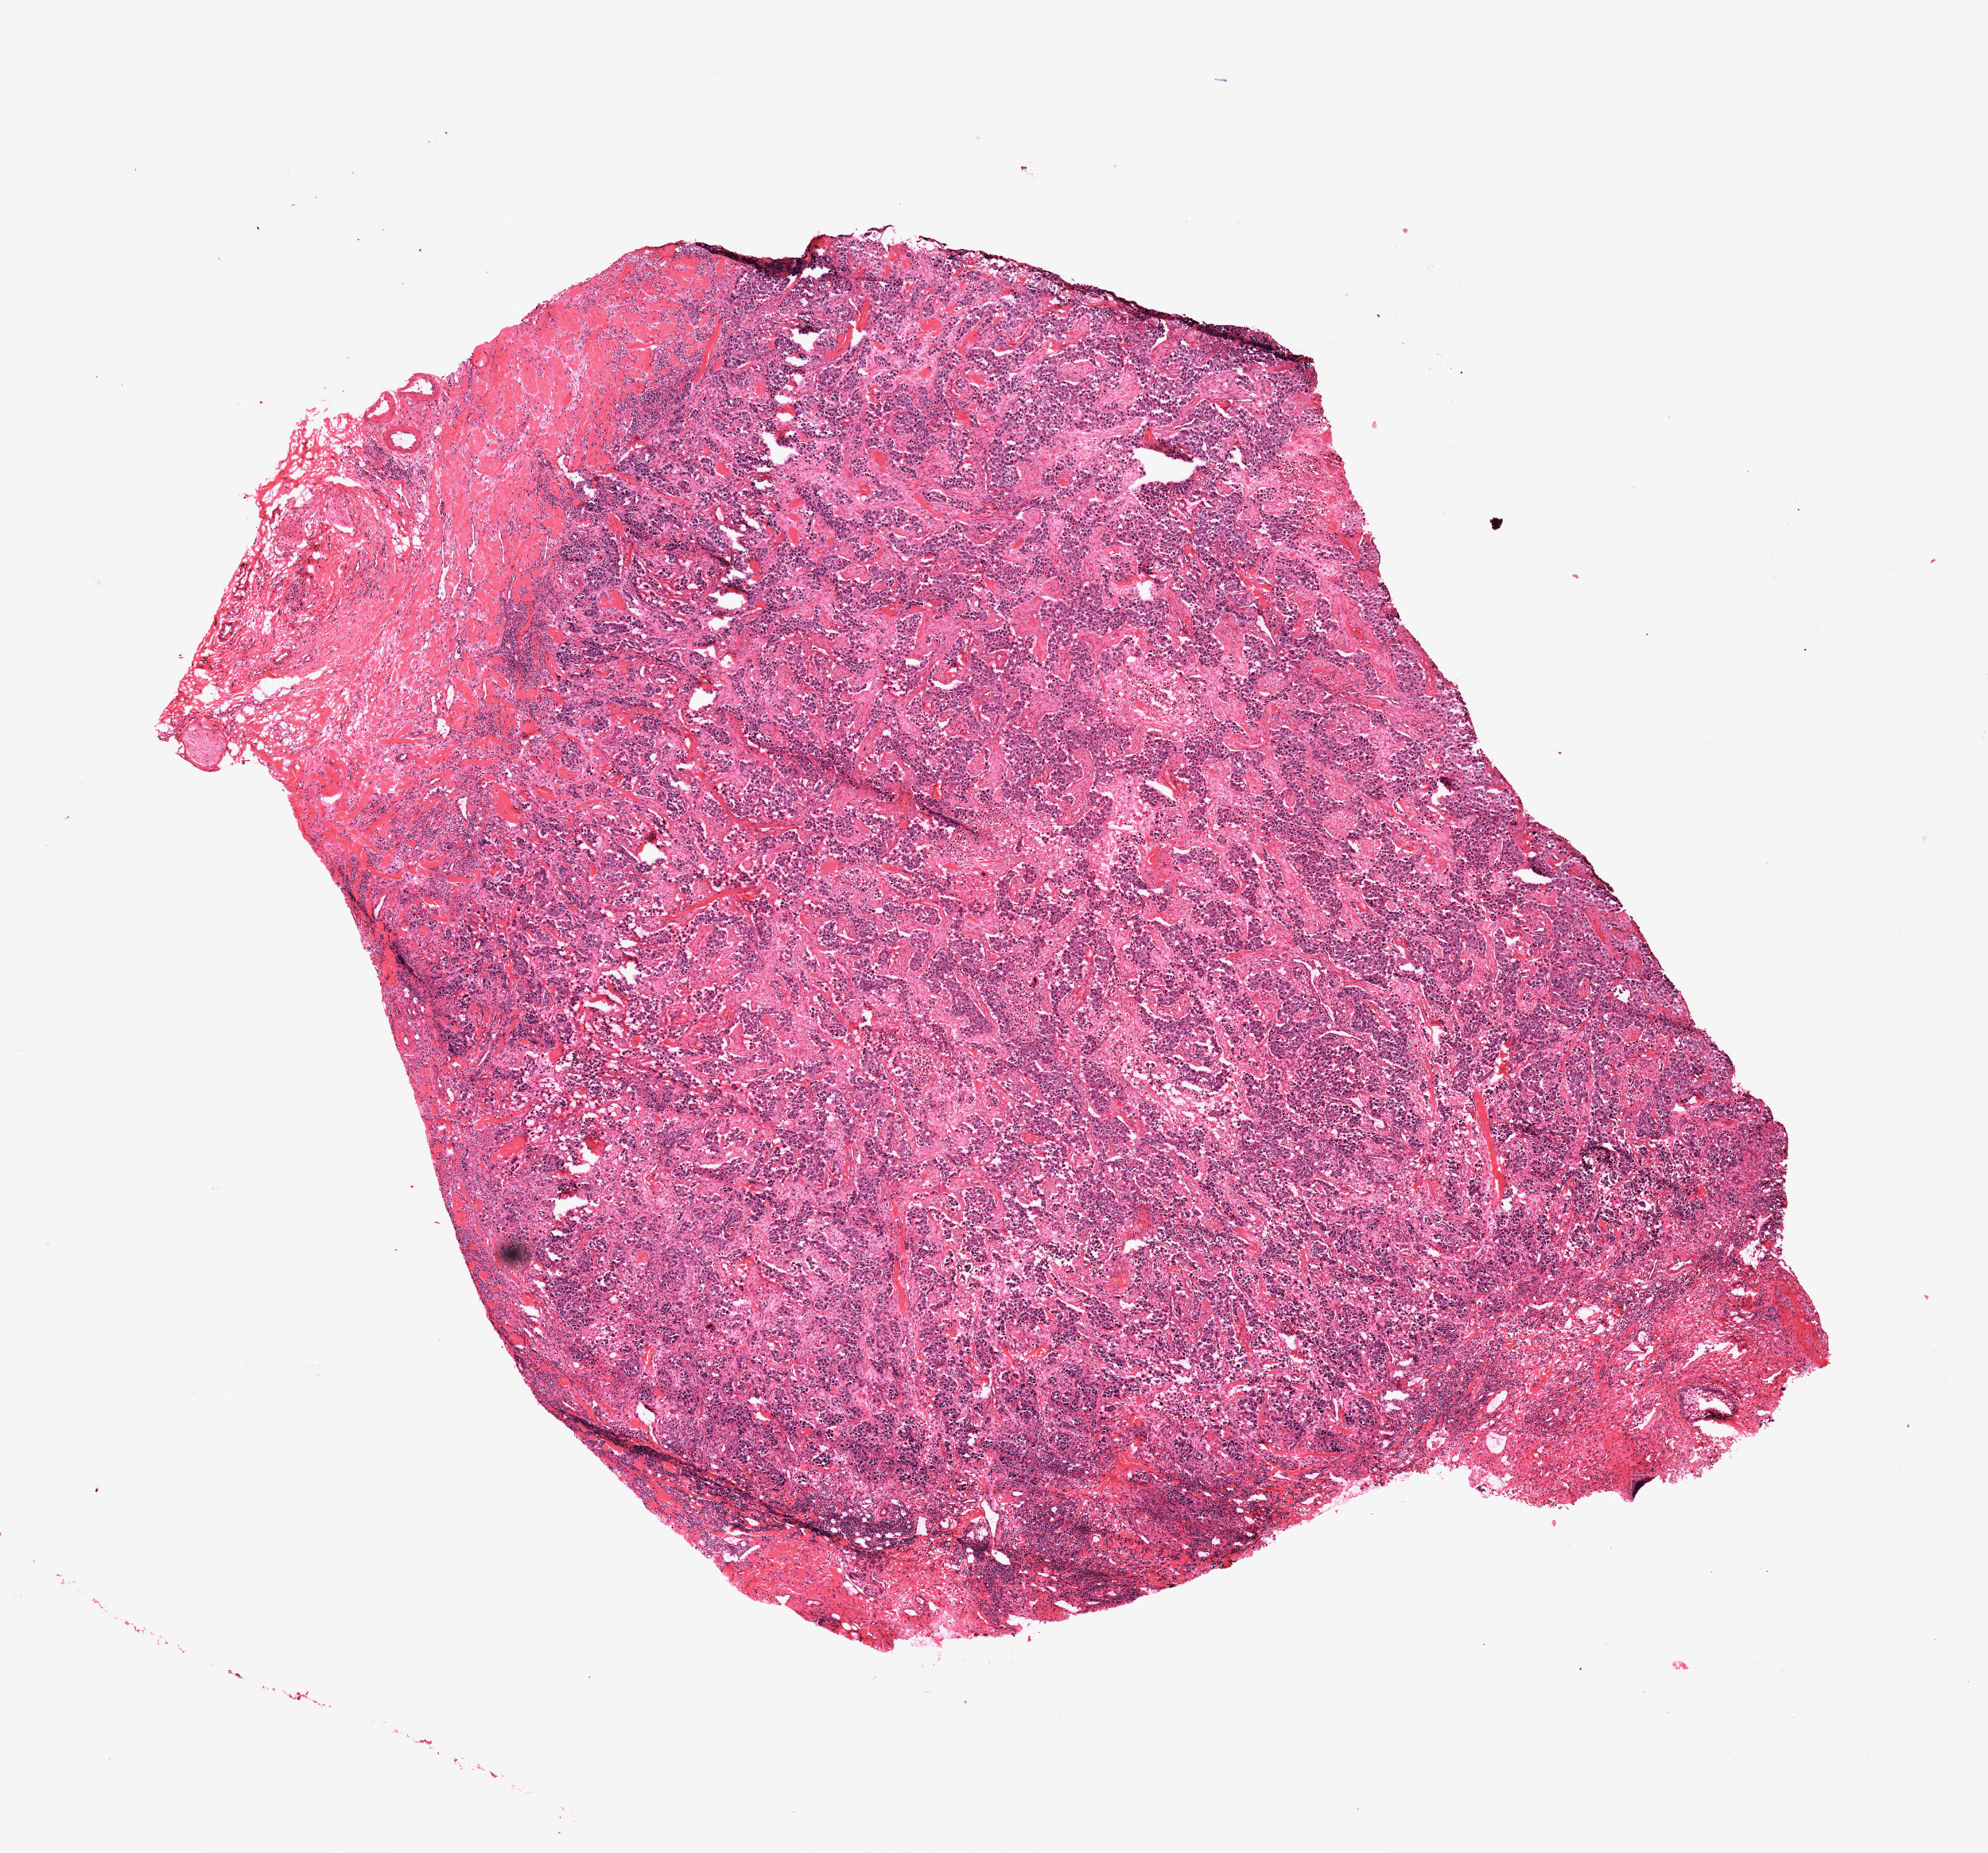
Hematoxylin and eosin (H&E) stained whole-slide image, whole scanned area (about 10.0 x 9.3 mm, from a 20x scan) shown as a low-resolution overview; formalin-fixed paraffin-embedded (FFPE) diagnostic section; head and neck, primary tumour sample. Male, age 74 years at initial diagnosis. Histologic grade: G3 (poorly differentiated).
Laterality: midline. AJCC pathologic stage: IVA. Diagnosis: Squamous cell carcinoma, NOS (floor of mouth, NOS).